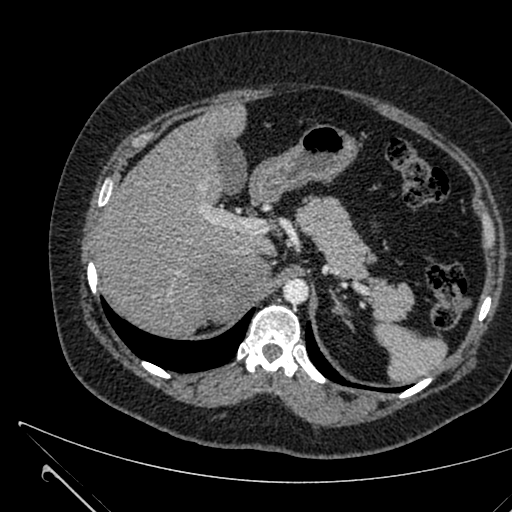
Contrast-enhanced abdominal CT, one axial slice. Position 464 of 731 along the scan axis. 120 kVp. Intravenous contrast given. Soft-tissue window (W 400 / L 40 HU). 1 mm slice thickness. 512 × 512 image matrix. Patient: female, 36 years. Case-level facts recorded for this patient, not image findings: diagnosis: adrenocortical carcinoma; tumour side: right adrenal; tumour size at pathology: 10 cm; Ki-67 index: 20 %; stage (as recorded): 4.
Annotated regions visible in this slice (semi-automatically segmented with operator editing):
- mass: bounding box <199,255,268,321> (left, top, right, bottom; pixels)